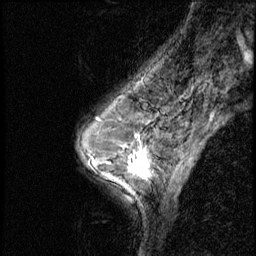
Breast MRI (dynamic contrast-enhanced), one sagittal slice. Position 37 of 56 along the scan axis. Dynamic contrast-enhanced series, image 2 of 3 at this slice position (ordered by acquisition). 1.5 T. TE 4.2 ms, TR 8.7 ms. 2.5 mm slice thickness. 256 × 256 image matrix. Female patient, age 50 years. From the clinical record (not read from this slice): setting: breast cancer imaged before/during neoadjuvant chemotherapy; receptor status: HR-positive, HER2-negative.
Structures marked on this image (semi-automatically segmented with operator editing):
- analysis volume of interest (the breast-tissue region the enhancement analysis was run in; not a lesion): box from (x=119, y=136) to (x=169, y=190) px
- tumour enhancement mask (voxels above the 140 % enhancement threshold inside the analysis volume of interest): (x=128, y=143)–(x=148, y=175)